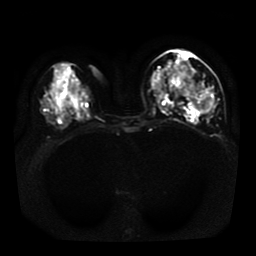
Breast MRI, one axial slice; slice 19 of 41 in the series (ordered by position); diffusion-weighted series; image 2 of 4 stored at this slice position (different b-values; order by instance number); 1.5 T; 256 × 256 image matrix, field of view 330 × 330 mm. Female patient.
Outlined on this slice (manually delineated by an expert):
- tumour on diffusion-weighted imaging: bounding box [x1, y1, x2, y2] px = [174, 85, 212, 110]